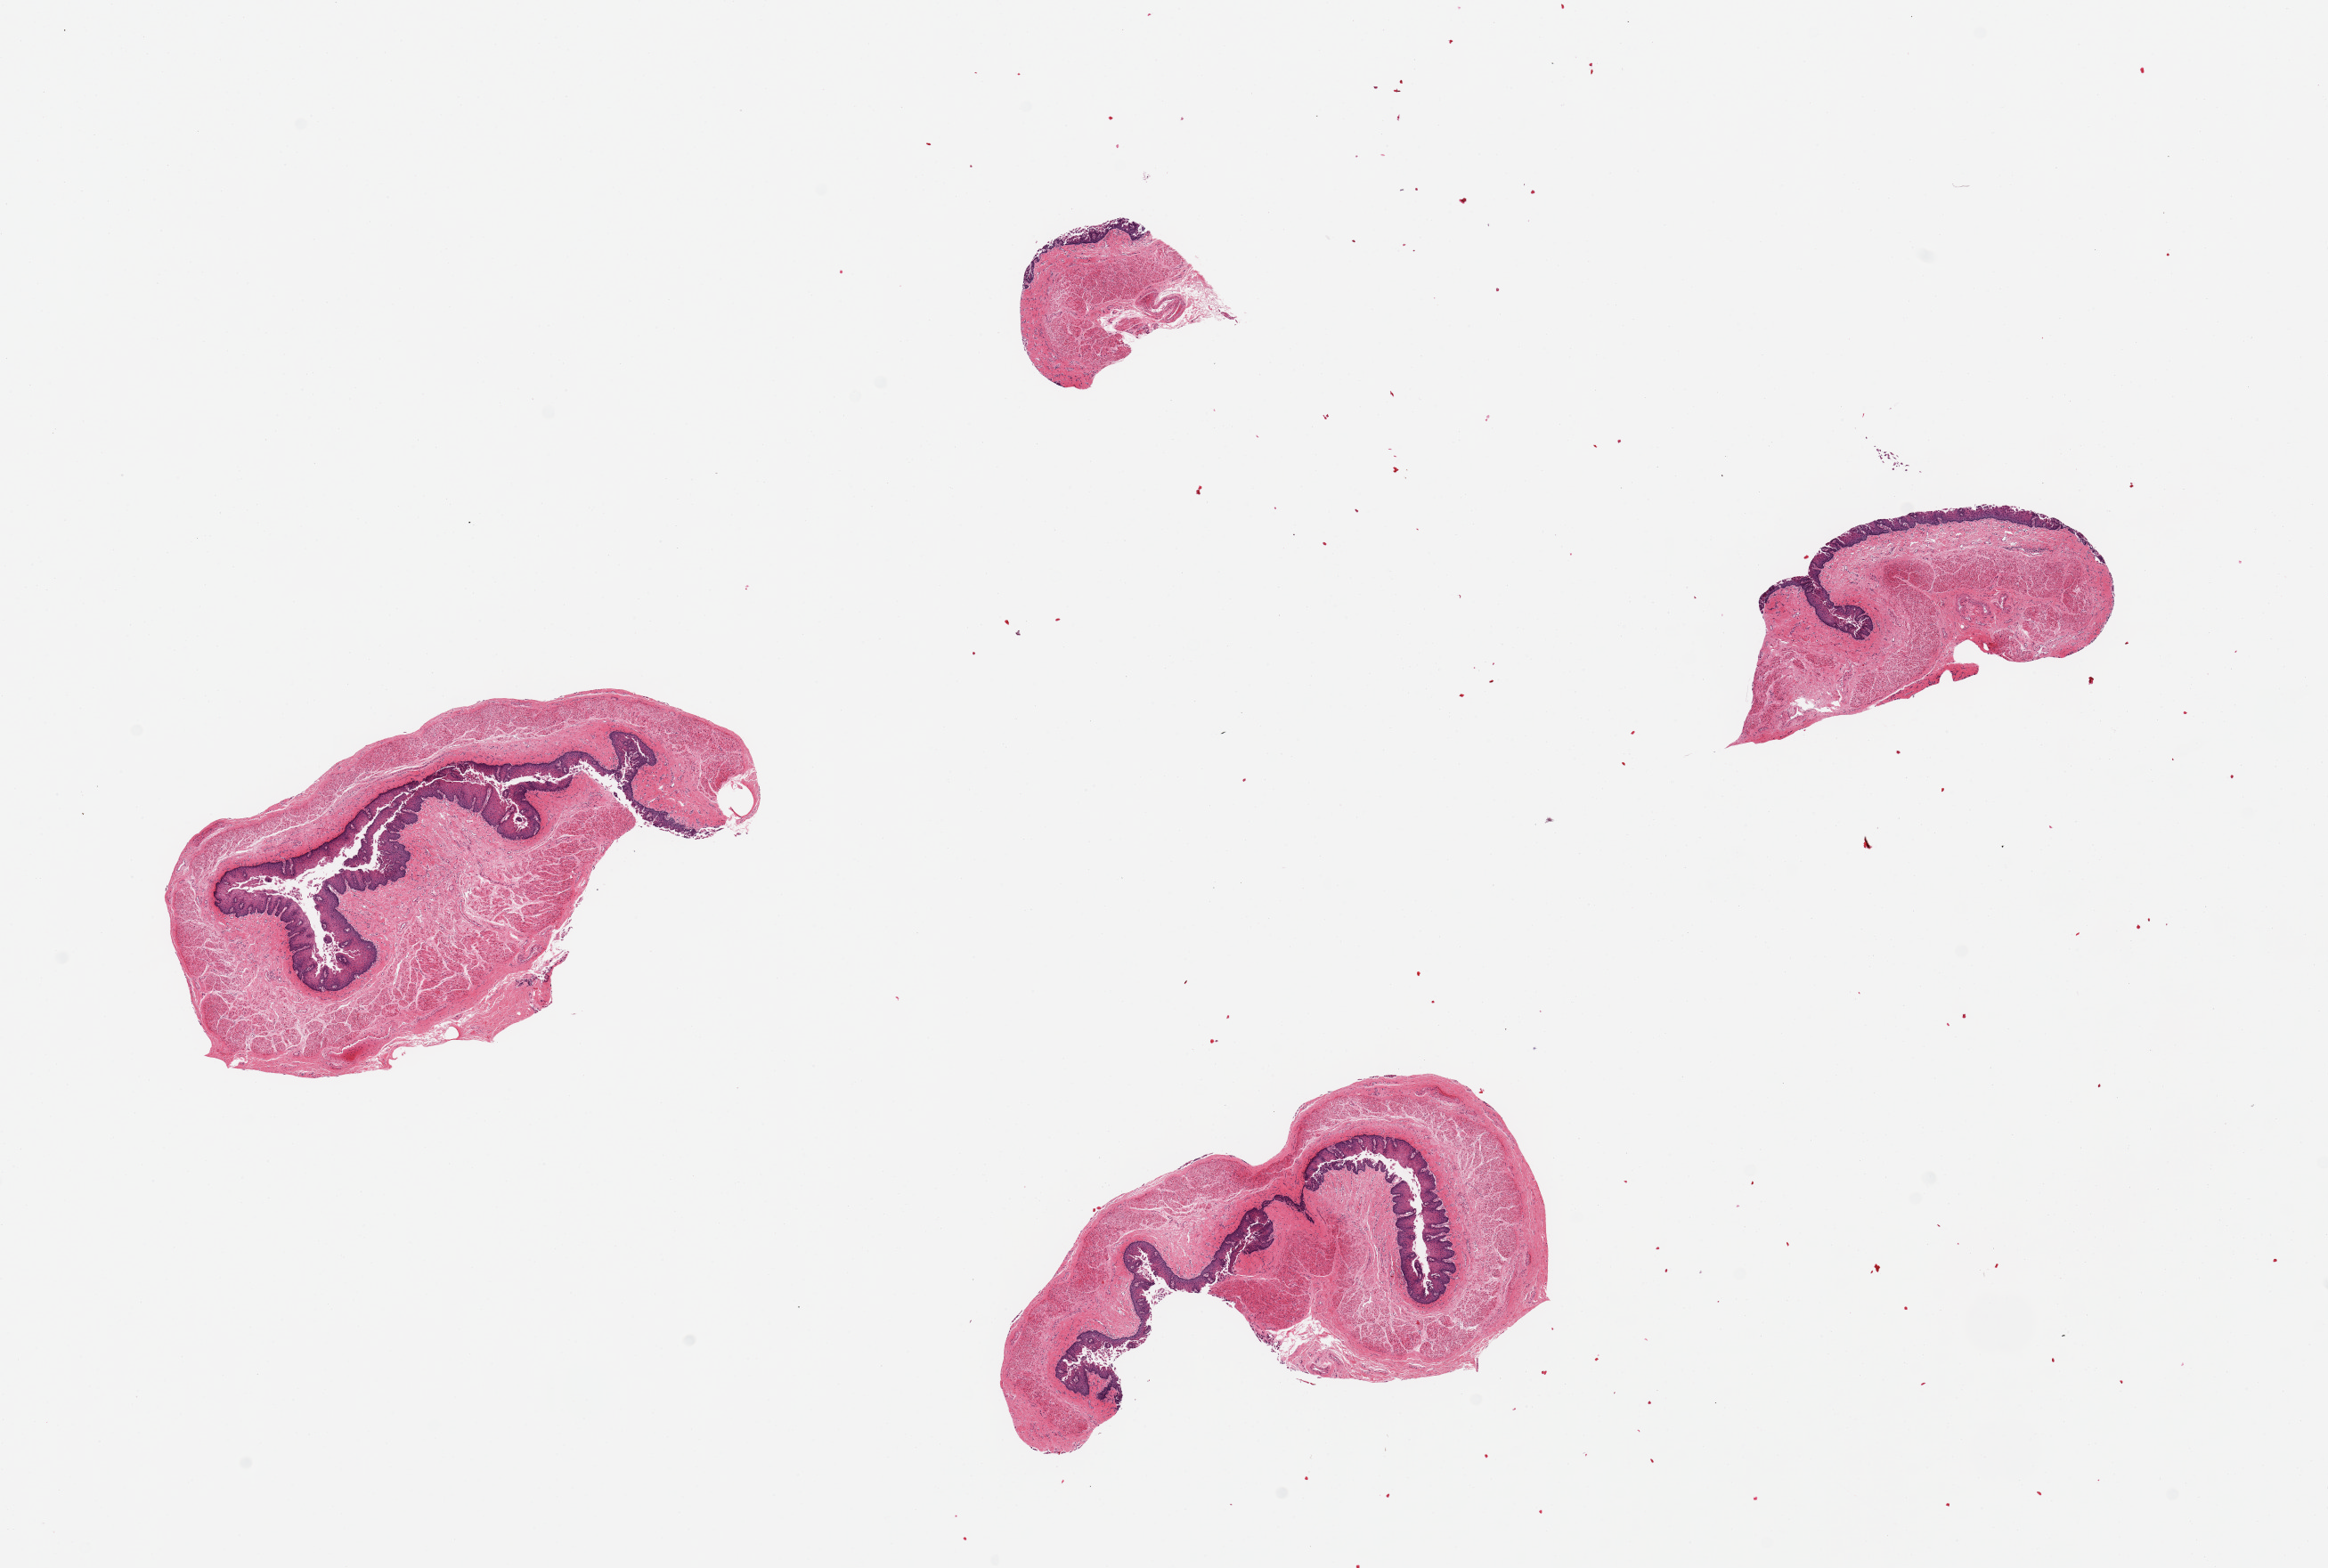
H&E whole-slide image, whole scanned area (about 20.7 x 13.9 mm) shown as a low-resolution overview, PAXgene-fixed paraffin-embedded (PFPE) section, sampled site (target tissue): esophageal mucous membrane, tissue donor sample. Donor: male.
- reviewer comment on this tissue sample: 4 pieces